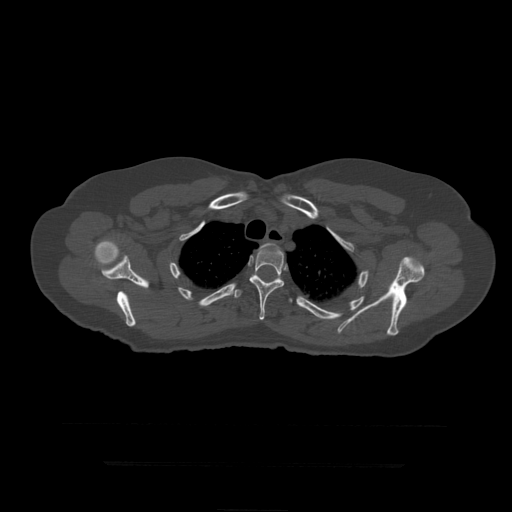
CT including the spine, one axial slice; position 349 of 399 along the scan axis; reconstruction kernel STANDARD; bone window (W 1800 / L 400 HU); 1.25 mm slice thickness; 512 × 512 image matrix, field of view 450 × 450 mm. Patient age 41 years. Case-level facts recorded for this patient, not image findings: primary cancer: breast.
Annotated regions visible in this slice (semi-automatic segmentation, software-assisted and operator-edited):
- T3 vertebra: box from (x=258, y=243) to (x=279, y=252) px
- T4 vertebra: (x=249, y=243)–(x=285, y=320)
- T5 vertebra: (x=235, y=282)–(x=293, y=303)